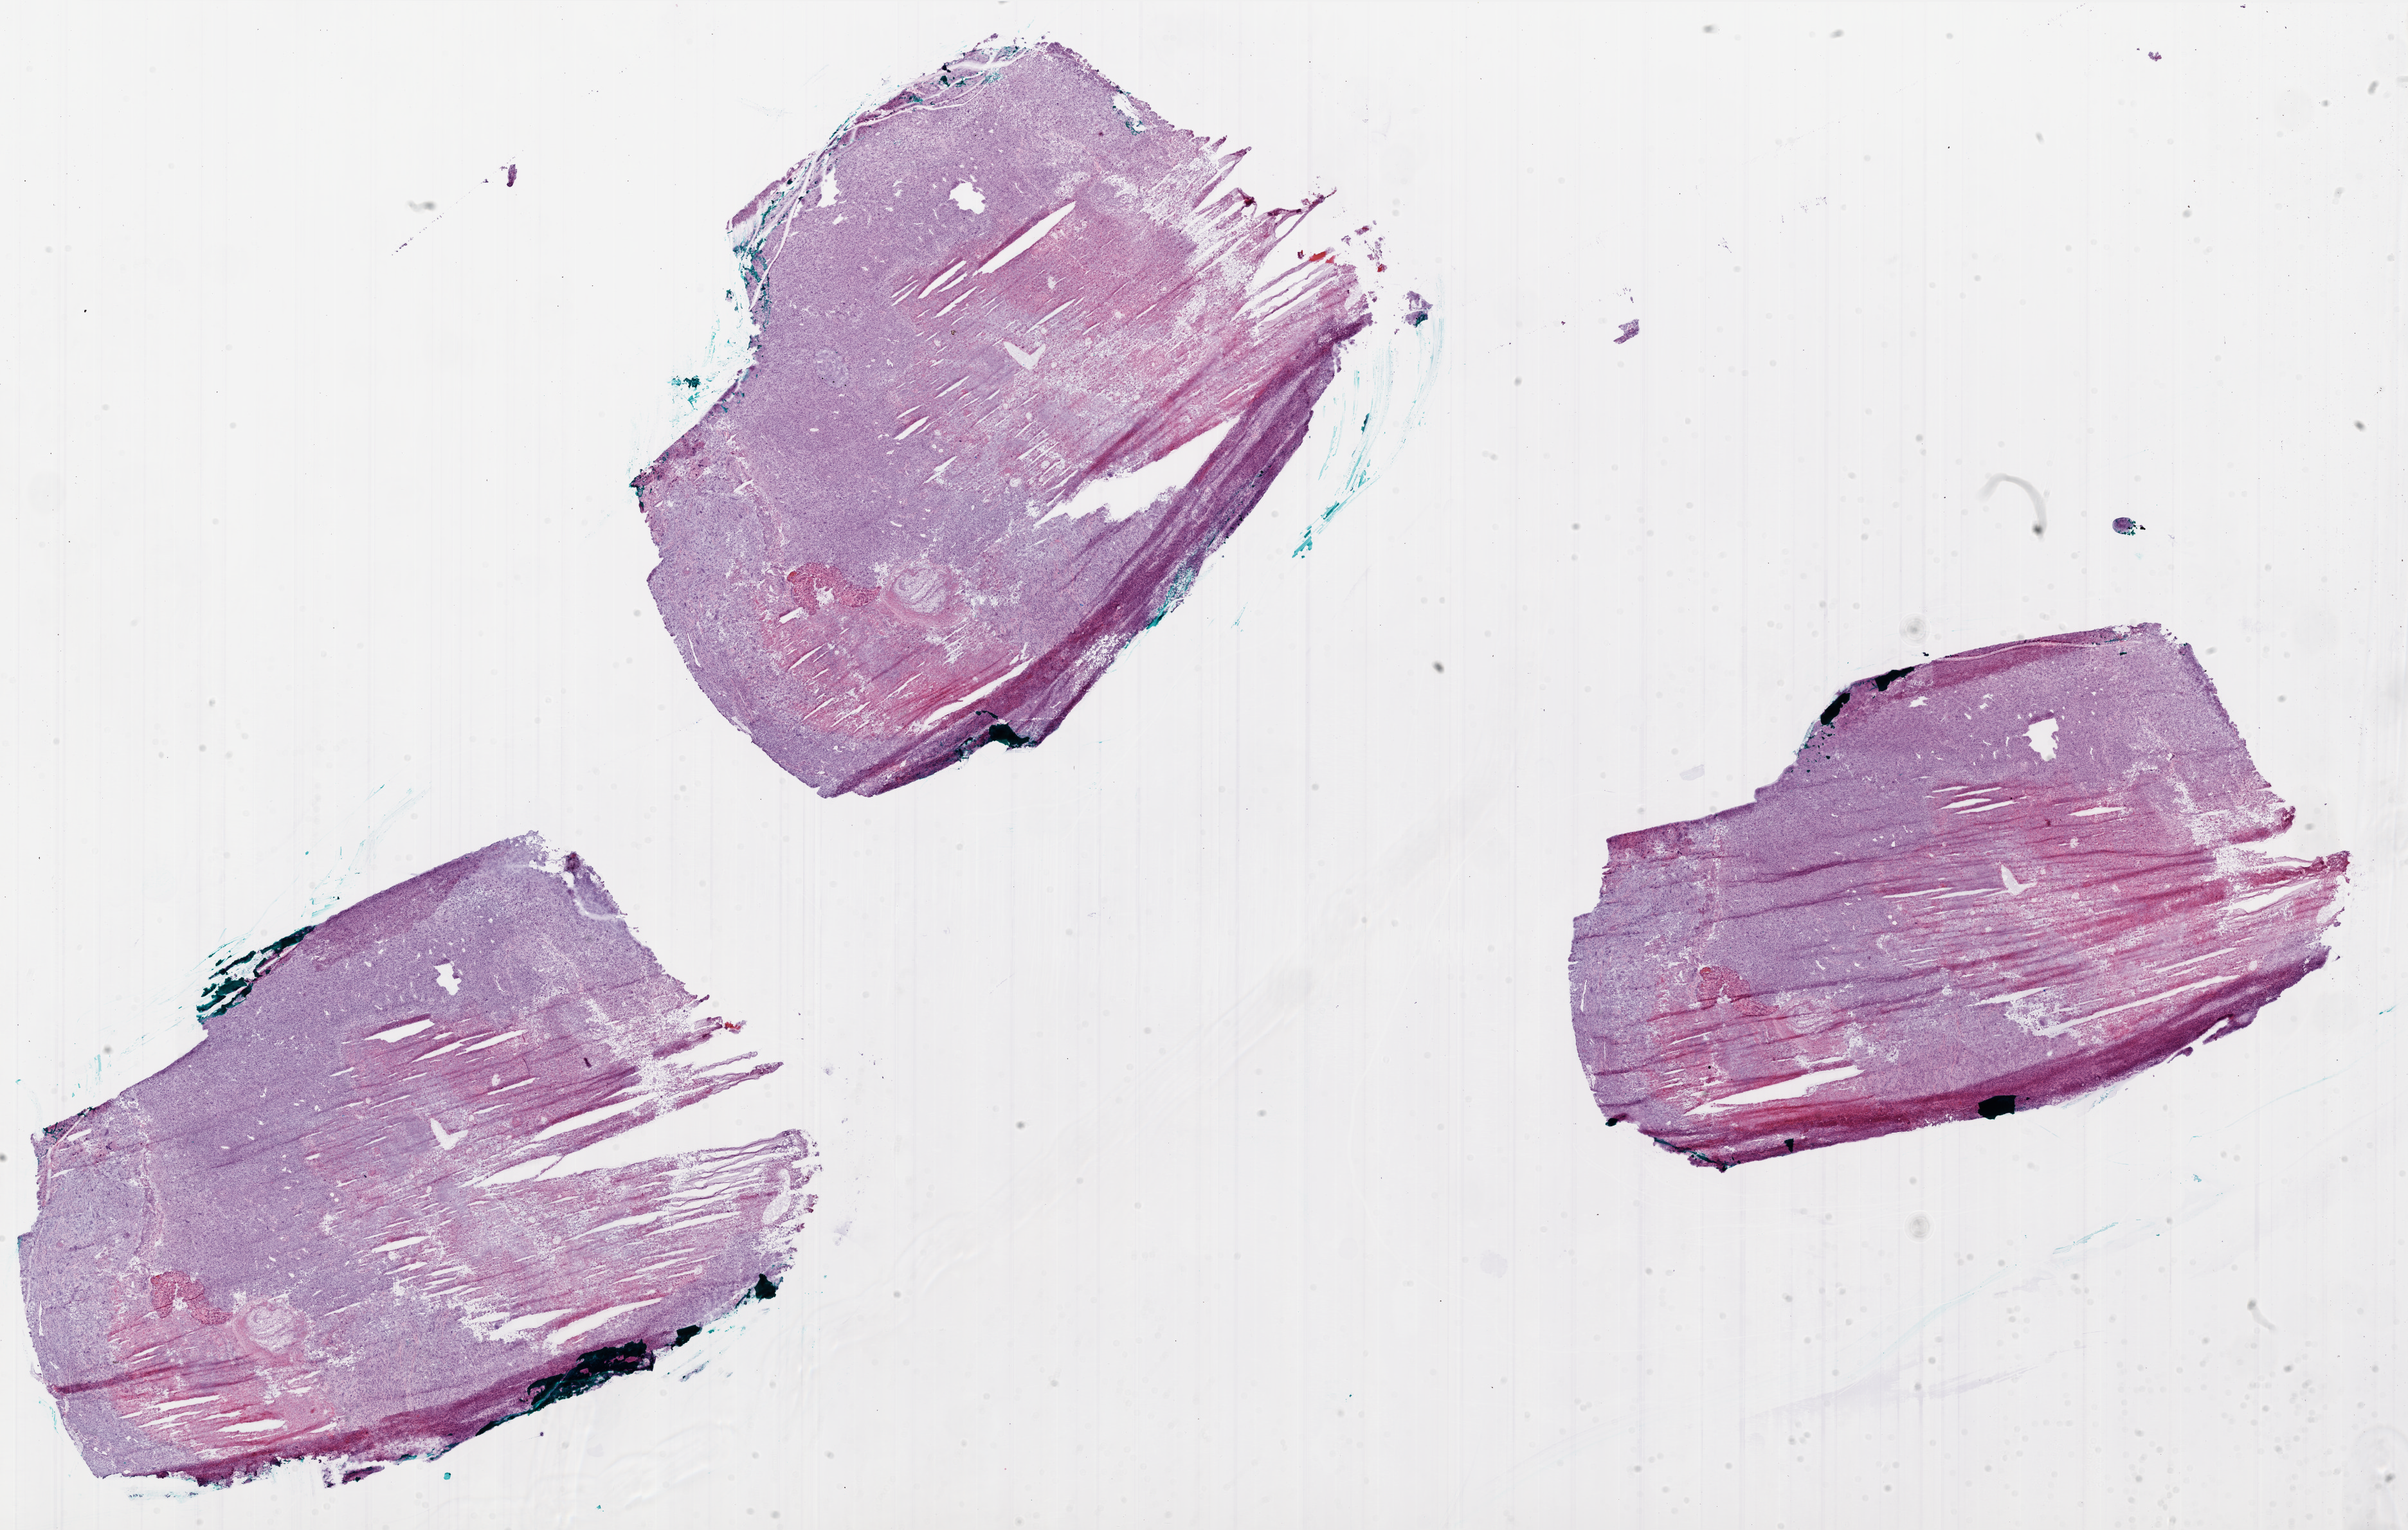
Hematoxylin and eosin (H&E) stained whole-slide image — a low-resolution overview of the entire scanned area, about 30.0 x 19.0 mm; frozen section; primary tumour sample from the brain. Male, age 34 years at initial diagnosis.
Histologic diagnosis: Glioblastoma.